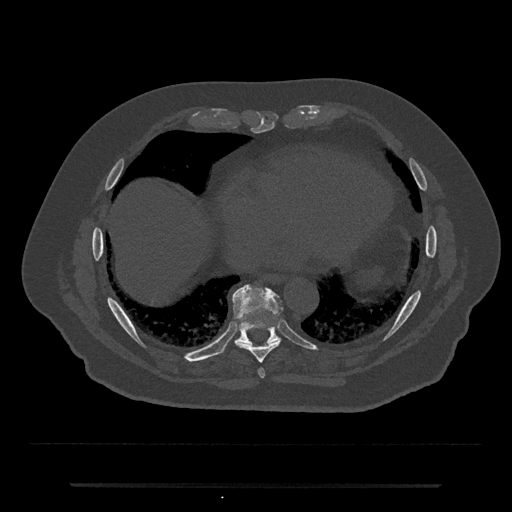
CT including the spine, one axial slice. Slice 787 of 797 in the series (ordered by position). Bone window (W 1800 / L 400 HU). 0.5 mm slice thickness. 512 × 512 image matrix, field of view 434 × 434 mm. Patient: male, 80 years. Case-level facts recorded for this patient, not image findings: primary cancer: prostate; vertebrae with lytic lesions (as recorded): L1, T11.
Structures marked on this image (semi-automatically segmented with operator editing):
- T8 vertebra: box from (x=236, y=324) to (x=280, y=363) px
- T9 vertebra: (x=222, y=284)–(x=283, y=352)